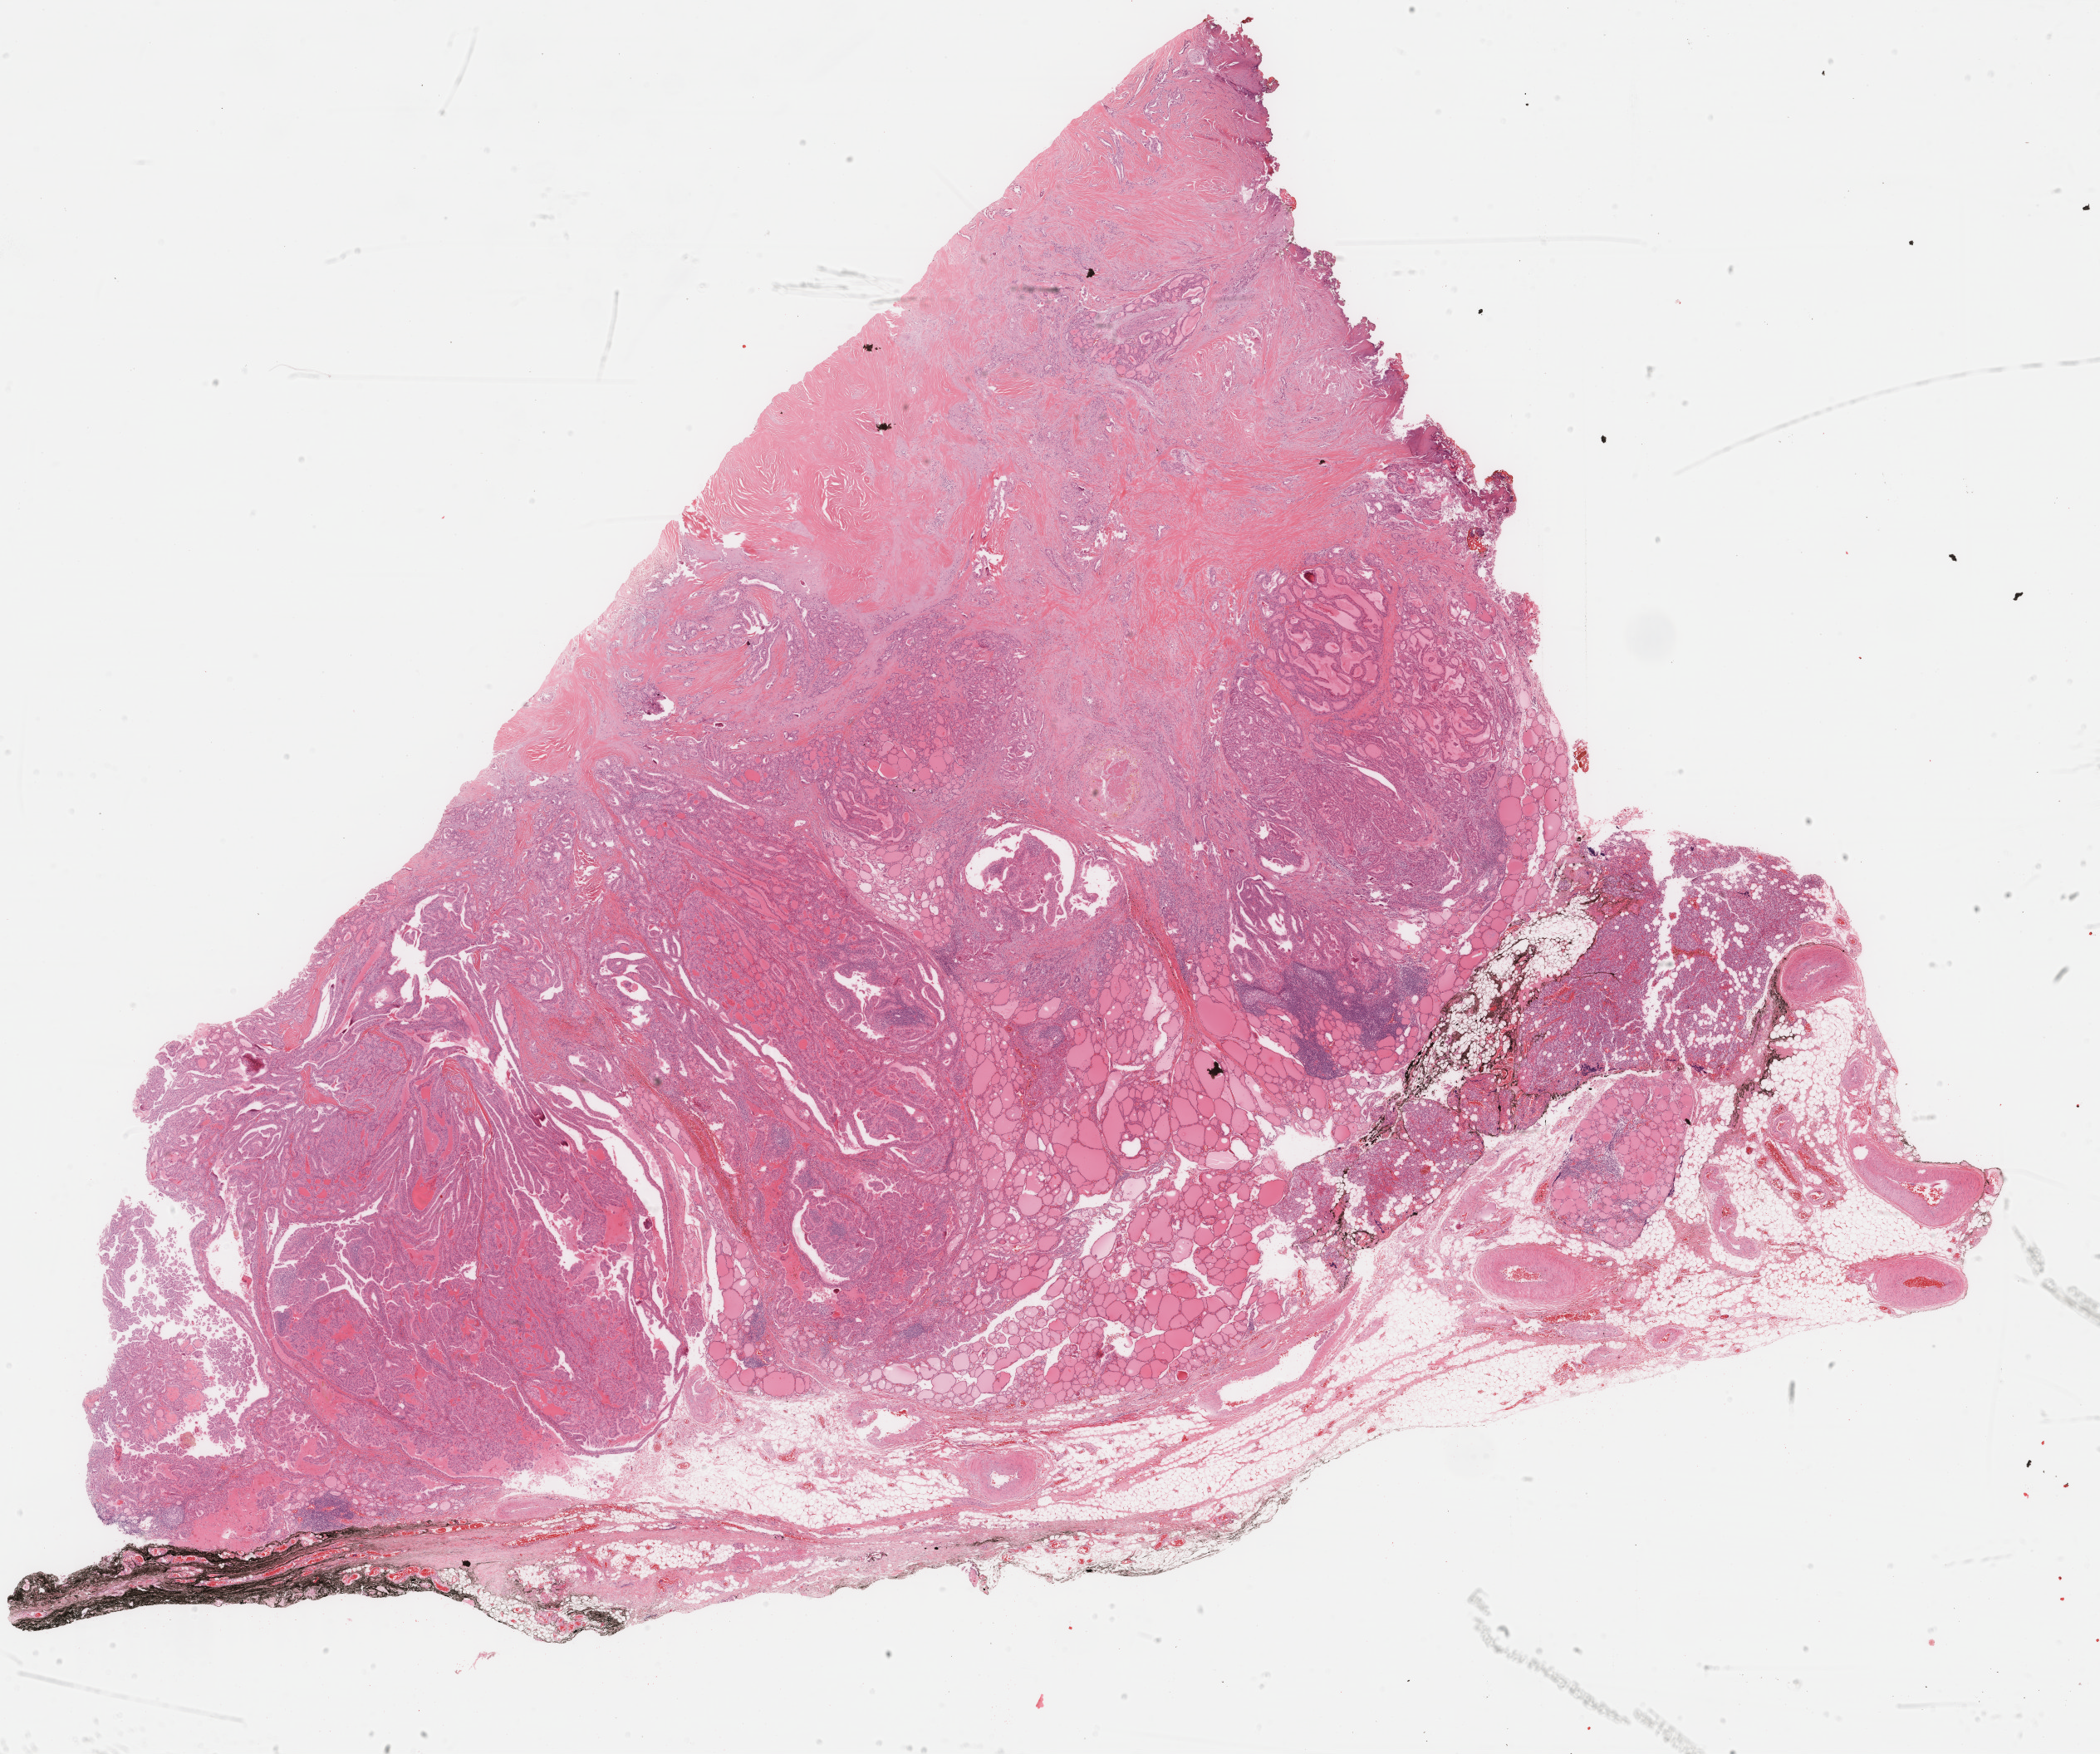
Whole-slide histology image, H&E, whole scanned area (about 20.1 x 16.8 mm, slide scanned at 40x) shown as a low-resolution overview. Formalin-fixed paraffin-embedded (FFPE) diagnostic section. Thyroid, primary tumour sample. Female patient.
Laterality: right. Lymph nodes positive (case pathology): 14 of 21 examined. Pathologic diagnosis: Papillary adenocarcinoma, NOS (thyroid gland). AJCC pathologic stage: III (5th edition).